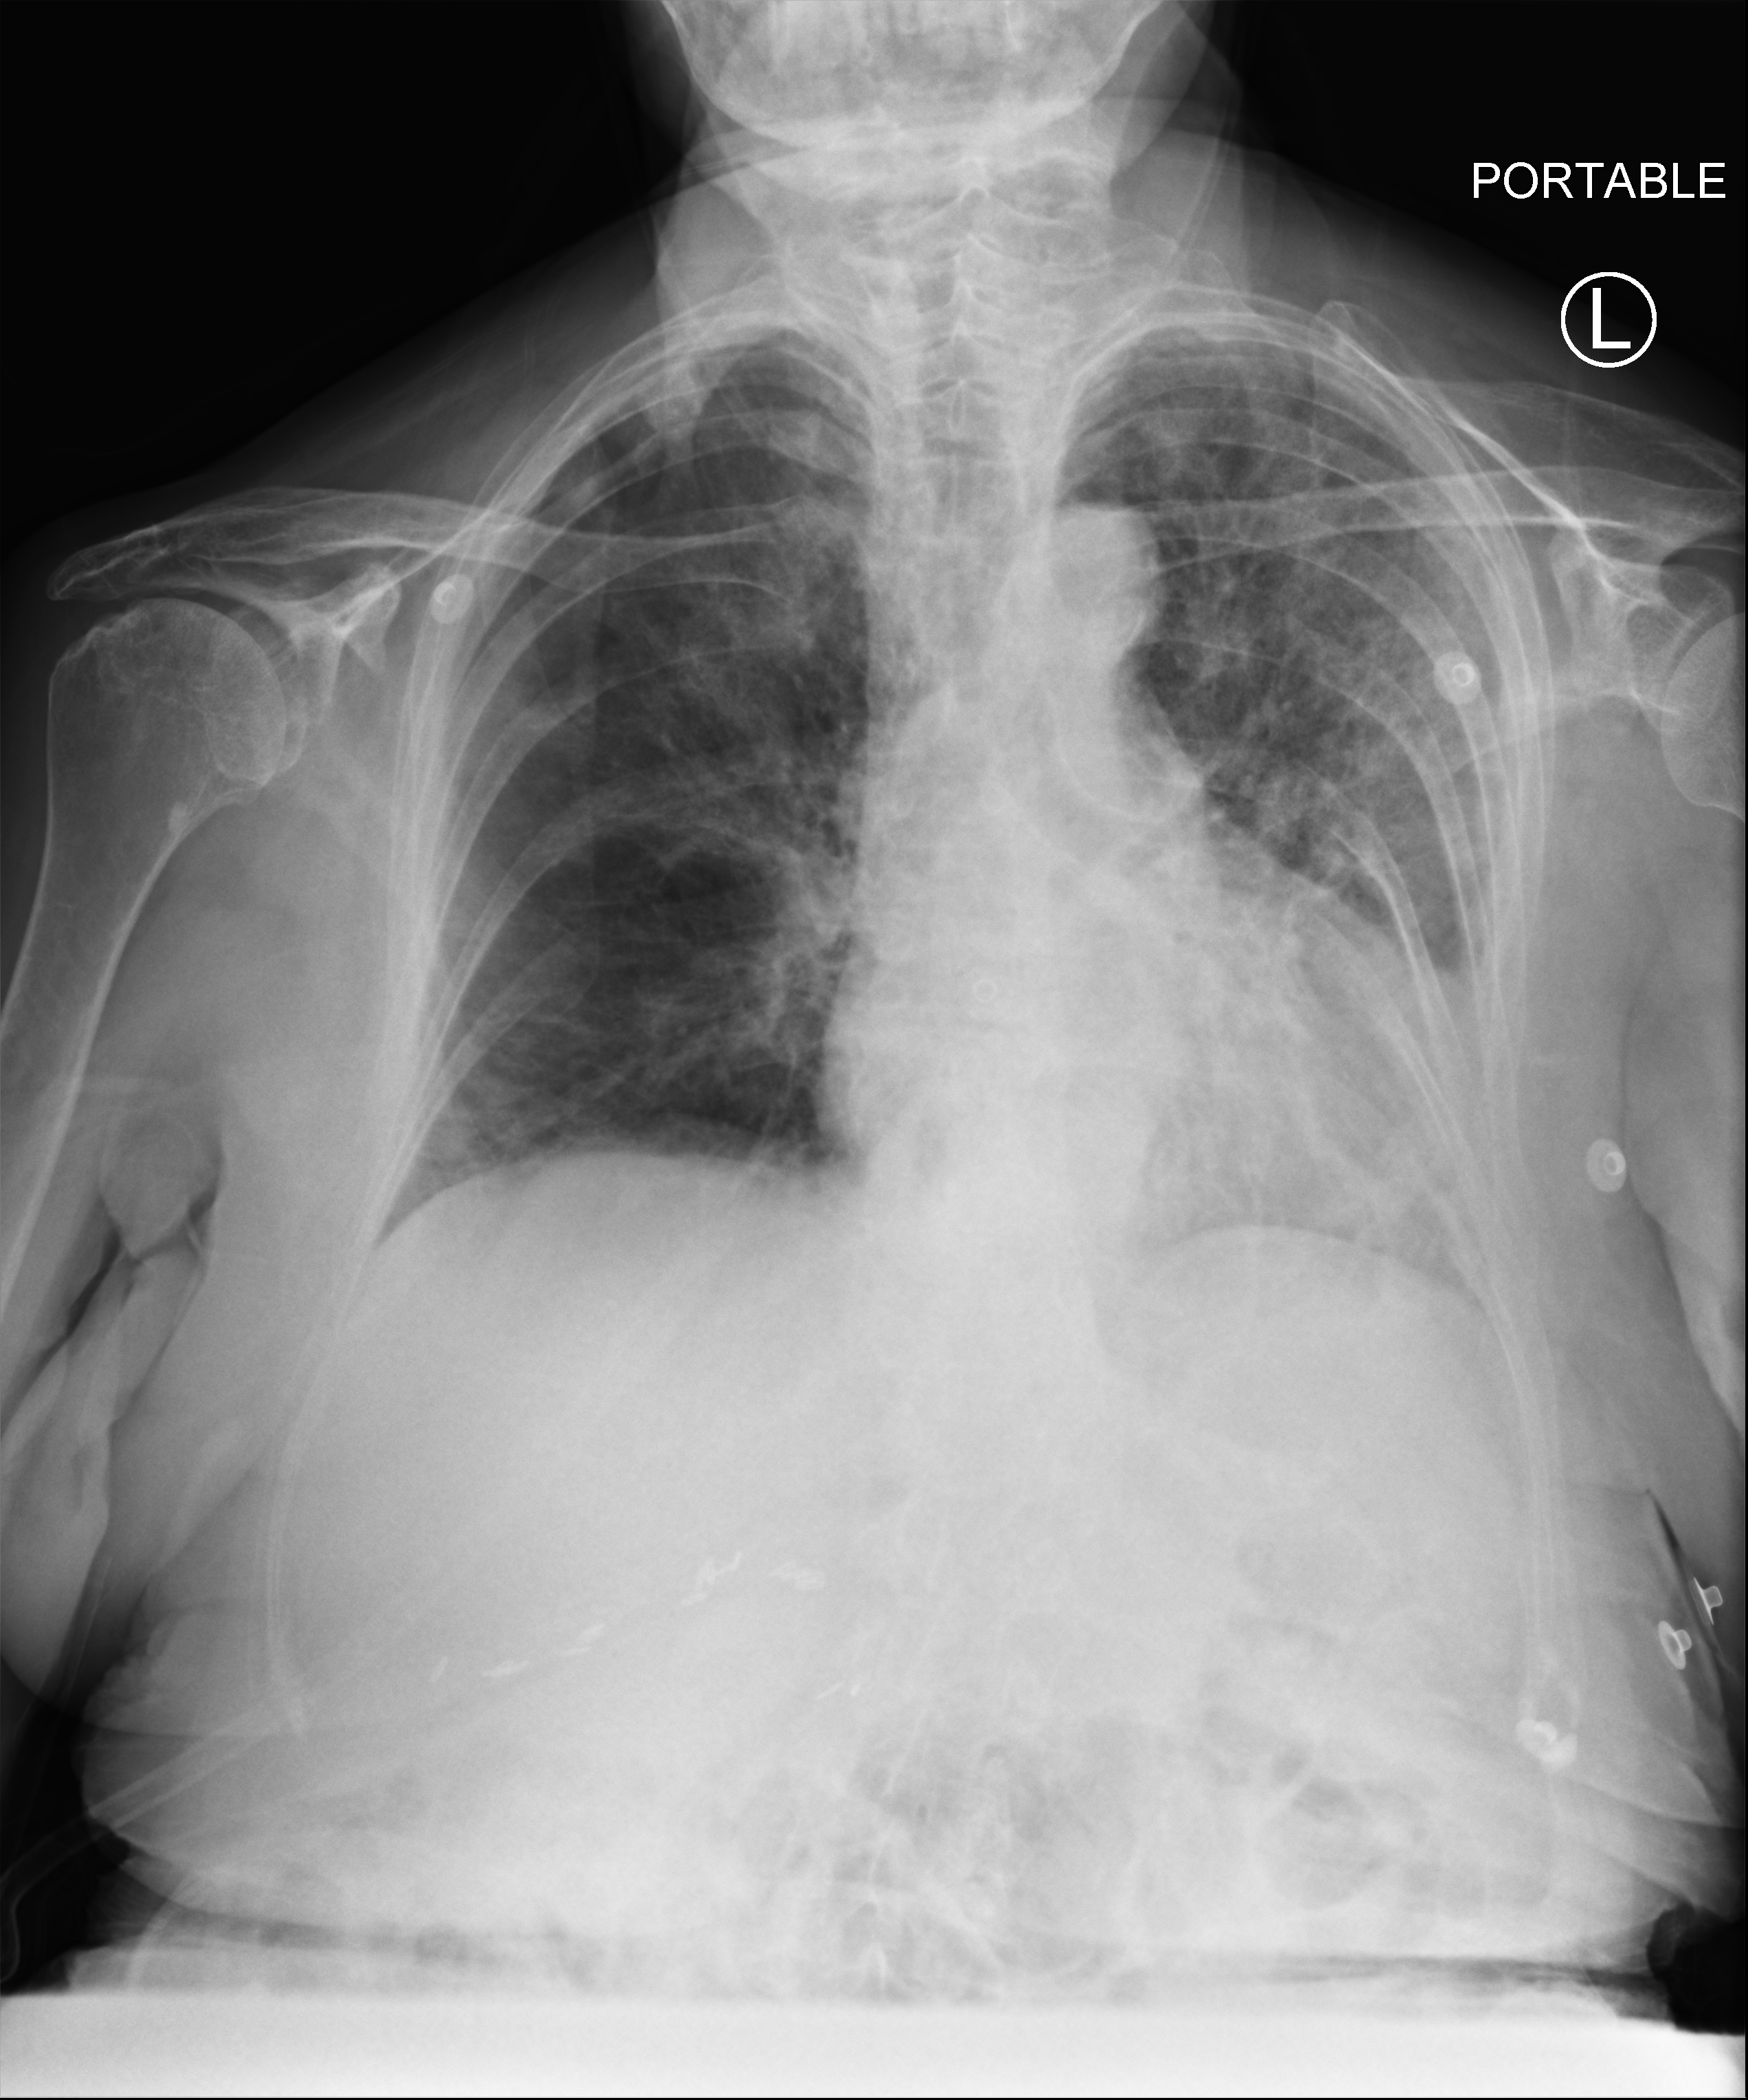
Portable chest radiograph. Patient hospitalised with COVID-19; female, aged 75–90 years.
Admission-level facts for this patient (not findings on this image; timing relative to this image not recorded):
- length of hospital stay: 26 days